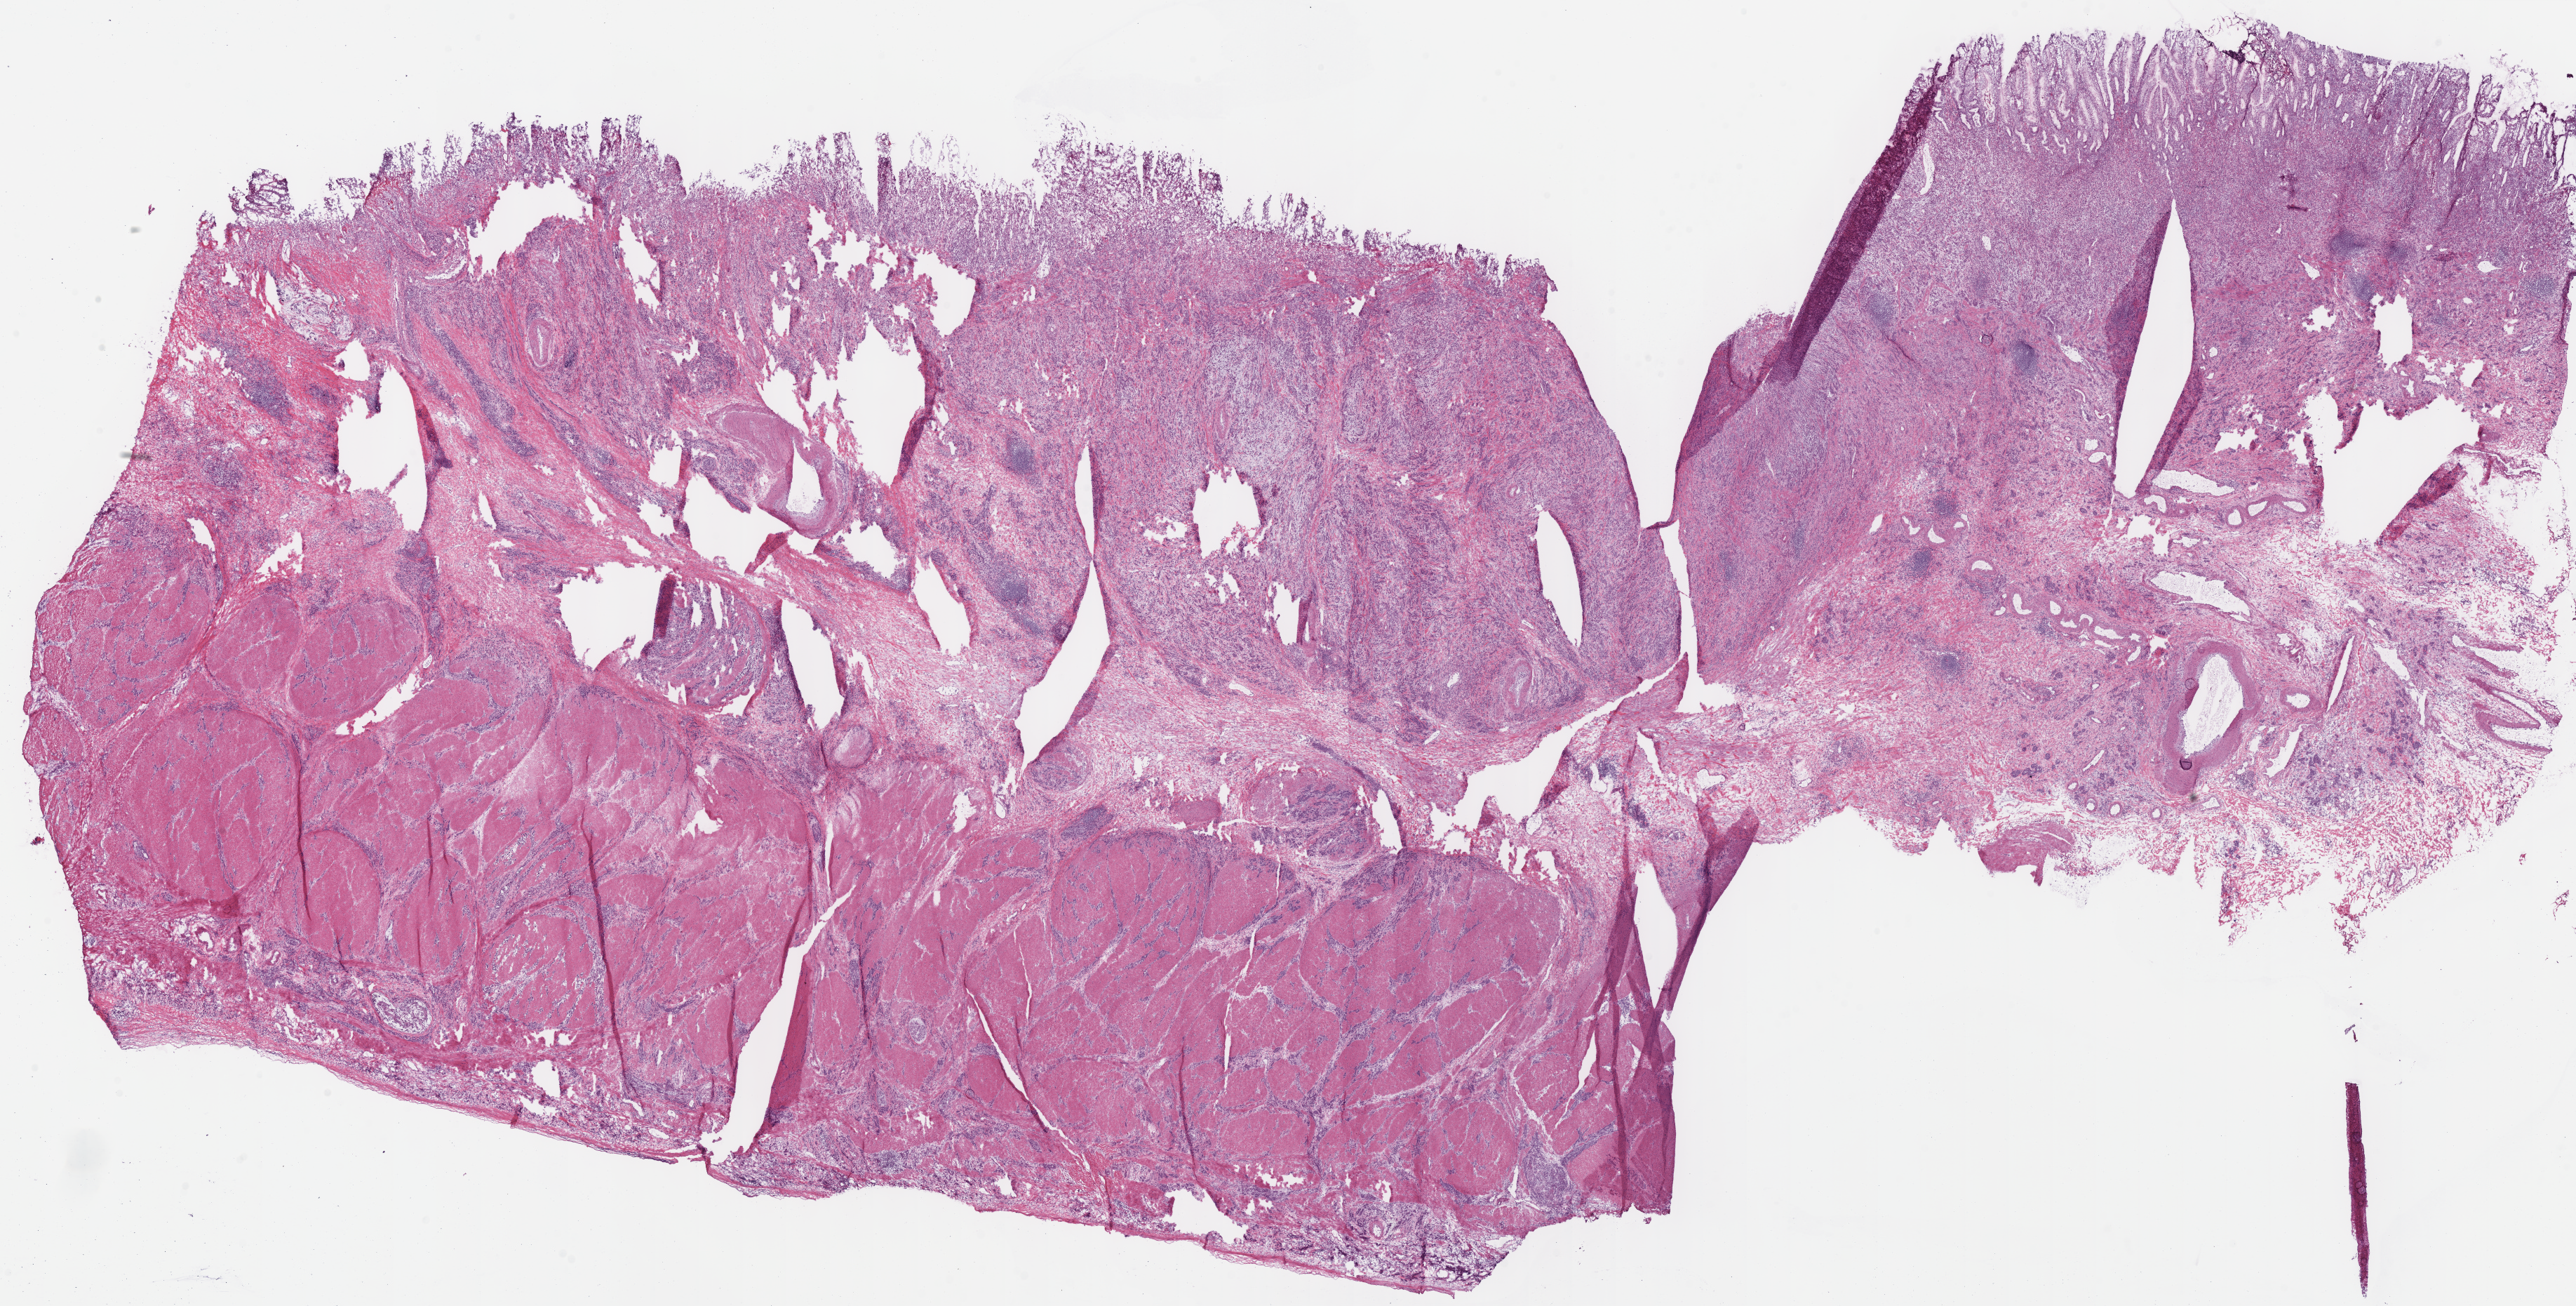
Digitized H&E-stained tissue section (whole slide), a low-resolution overview of the entire scanned area, about 28.9 x 14.6 mm, frozen section, stomach, primary tumour sample. Male, age 55 years at initial diagnosis. Histologic grade: G3 (poorly differentiated). Pathologist review of this section (percent, as recorded): tumour cells 90%, tumour nuclei 72%, normal cells 3%, stromal cells 7%, necrosis 0%. Infiltration values recorded for this section: lymphocyte infiltration 10%, monocyte infiltration 2%, neutrophil infiltration 10%.
* lymph nodes positive (case pathology): 11 of 15 examined
* diagnosis: Adenocarcinoma, NOS (gastric antrum)
* AJCC pathologic stage: IIIC (7th edition)